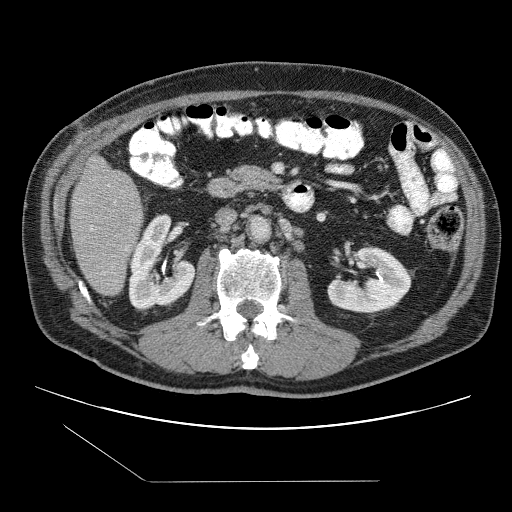
Contrast-enhanced abdominal CT (liver protocol), one axial slice; slice 28 of 109 in the series (ordered by position); reconstruction kernel STANDARD; 120 kVp; one of 2 acquisitions stored at this slice position; soft-tissue window (W 400 / L 40 HU); 2.5 mm slice thickness; 512 × 512 image matrix. Case-level facts recorded for this patient, not image findings: diagnosis: hepatocellular carcinoma (patient treated with transarterial chemoembolisation; whether this scan precedes or follows treatment is not stated here); TNM stage (as recorded): Stage-IIIB; Child-Pugh class: A.
Outlined on this slice (semi-automatically segmented with operator editing):
- liver parenchyma outside the tumour (the mass and vessels are separate outlines, so this box may not span the whole liver): bounding box [x1, y1, x2, y2] px = [70, 154, 142, 294]
- liver vessels: [91, 226, 93, 231]